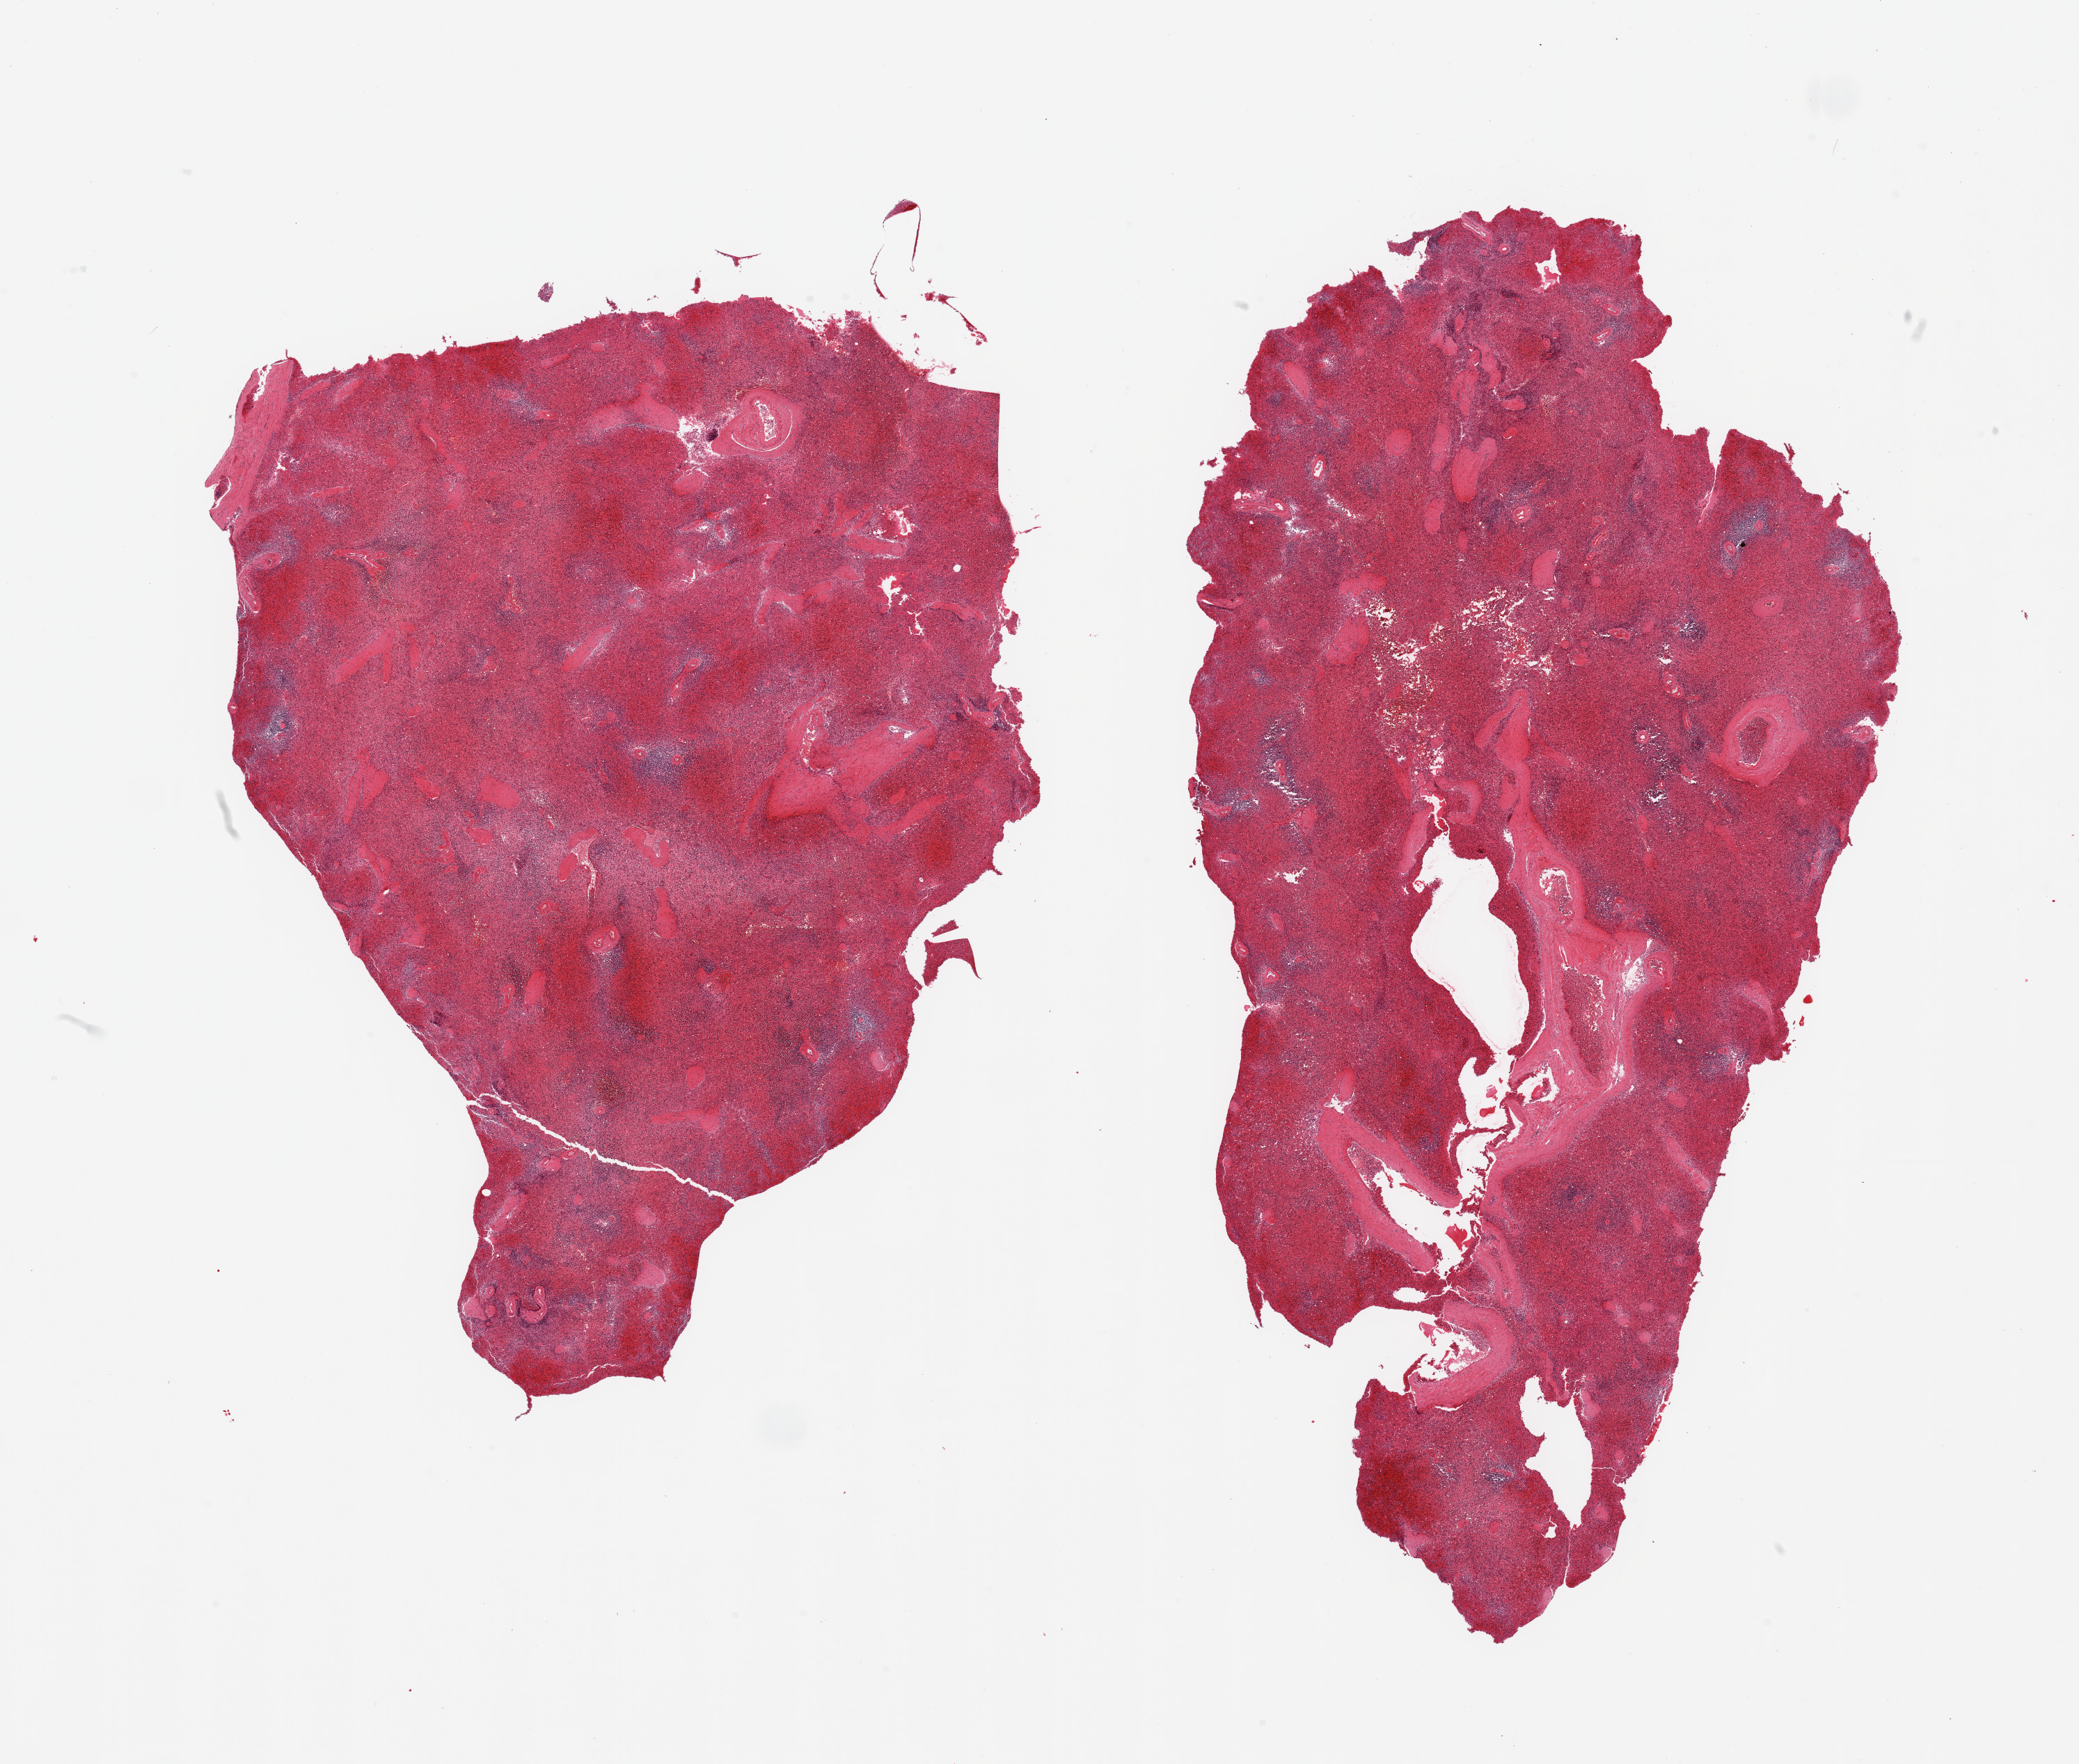
Whole-slide image, haematoxylin and eosin stain, shown as a low-resolution overview of the whole scanned area (about 23.6 x 20.0 mm). PAXgene-fixed, paraffin-embedded tissue. Target tissue: spleen. Tissue donor sample. Donor: male.
Pathologist's review note for this sample: 2 pieces, marked congestion, advanced autolysis.